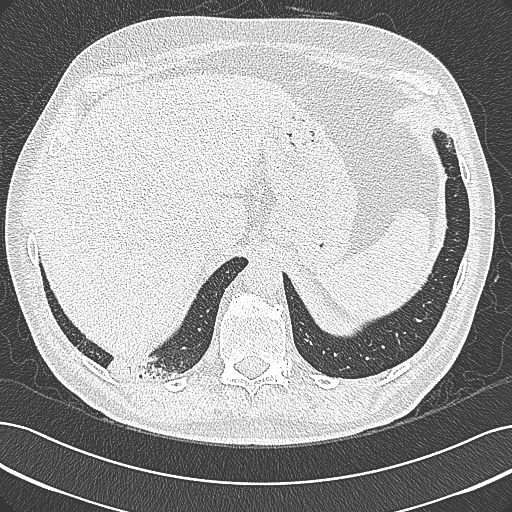
Low-dose screening chest CT, axial slice; baseline screening round; lung window (W 1500 / L -600 HU); 1 mm slice thickness; slice 261 of 355 in the series; 512 × 512 image matrix, field of view 362 × 362 mm. Male, age 68 years at enrolment. Former smoker at enrolment.
- Lesion marked by an expert reader, bounding box (x1, y1, x2, y2) in pixels: (93, 336, 196, 396).
- No non-calcified nodule or mass ≥4 mm was recorded by the screening reader at this exam.
- Official screen result: negative screen, significant abnormalities not suspicious for lung cancer.
- Later outcome: lung cancer diagnosed 154 days after this screen — mucinous adenocarcinoma, right lower lobe, well differentiated (G1), stage IB (AJCC 6th edition), 50 mm at pathology.